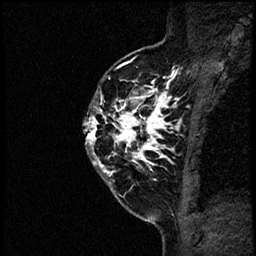
Breast MRI (dynamic contrast-enhanced), one sagittal slice. Position 43 of 60 along the scan axis. Dynamic contrast-enhanced study with each time point stored as its own series, time point 2 of 4 at this slice position (early post-contrast, ordered by acquisition time). 1.5 T. TE 4.2 ms, TR 17.6 ms. 2 mm slice thickness. 256 × 256 image matrix, field of view 200 × 200 mm. Patient: female, 40 years. Case-level facts recorded for this patient, not image findings: setting: breast cancer imaged before/during neoadjuvant chemotherapy; receptor status: HER2-positive.
Annotated regions visible in this slice (semi-automatic segmentation, software-assisted and operator-edited):
- analysis volume of interest (the breast-tissue region the enhancement analysis was run in; not a lesion): bounding box (x1, y1, x2, y2) in pixels: (84, 56, 197, 205)
- tumour enhancement mask (voxels above the 100 % enhancement threshold inside the analysis volume of interest): (85, 61, 189, 184)